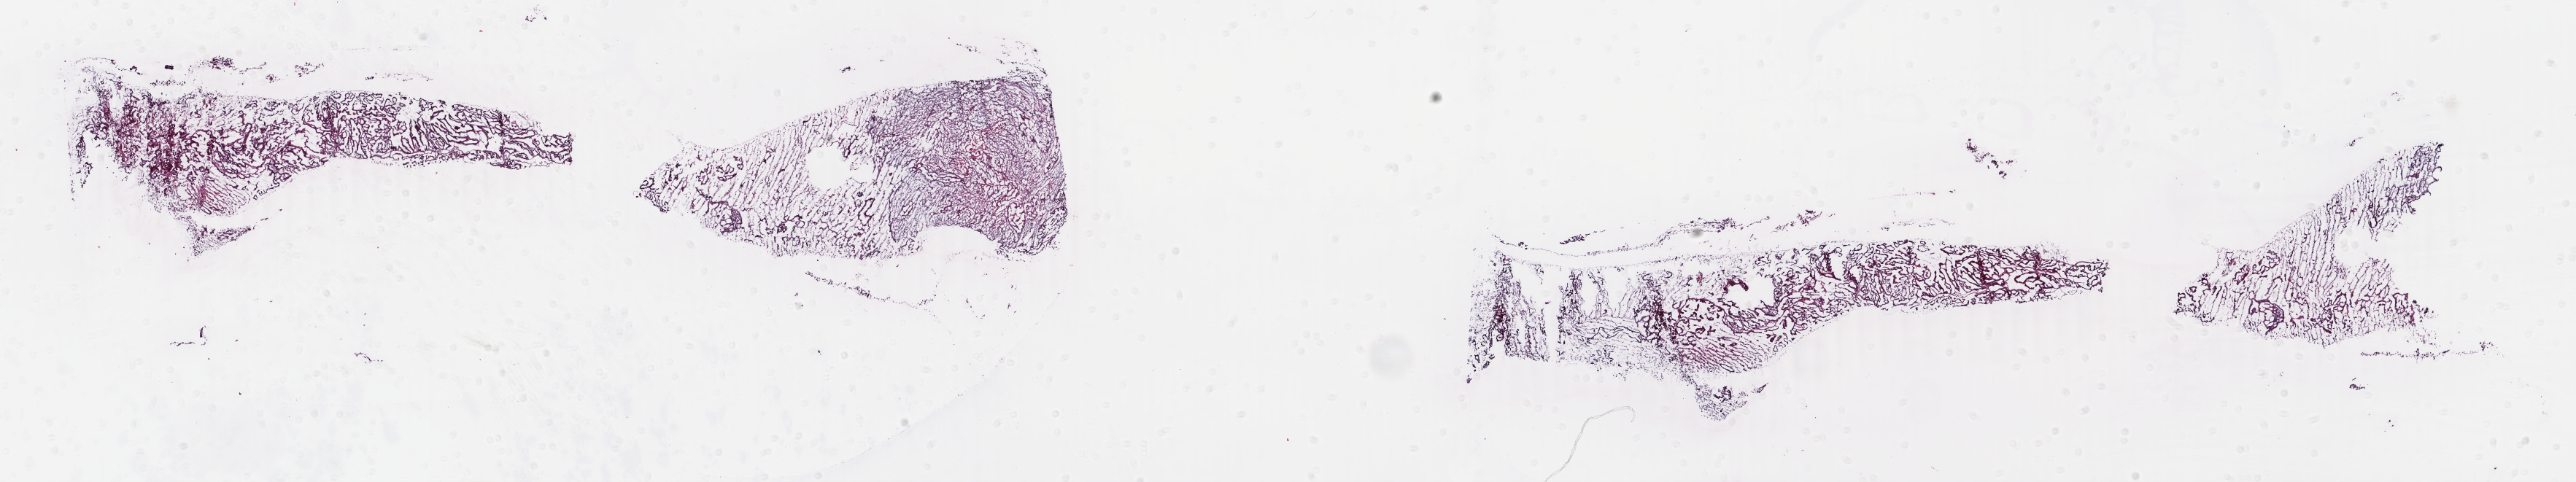
Hematoxylin and eosin (H&E) stained whole-slide image, whole scanned area (about 28.1 x 5.3 mm, slide scanned at 40x) shown as a low-resolution overview; frozen section from the top of the tissue portion; sample: primary tumour, uterus. Patient: female, age at initial diagnosis 82 years. Histologic grade: G2 (moderately differentiated). Pathologist review of this section (percent, as recorded): tumour cells 55%, tumour nuclei 60%, normal cells 15%, stromal cells 5%, necrosis 25%. Inflammatory infiltration, as recorded: lymphocyte infiltration 3%, monocyte infiltration 0%, neutrophil infiltration 0%.
* FIGO stage: IIIA
* diagnosis: Endometrioid adenocarcinoma, NOS (endometrium)